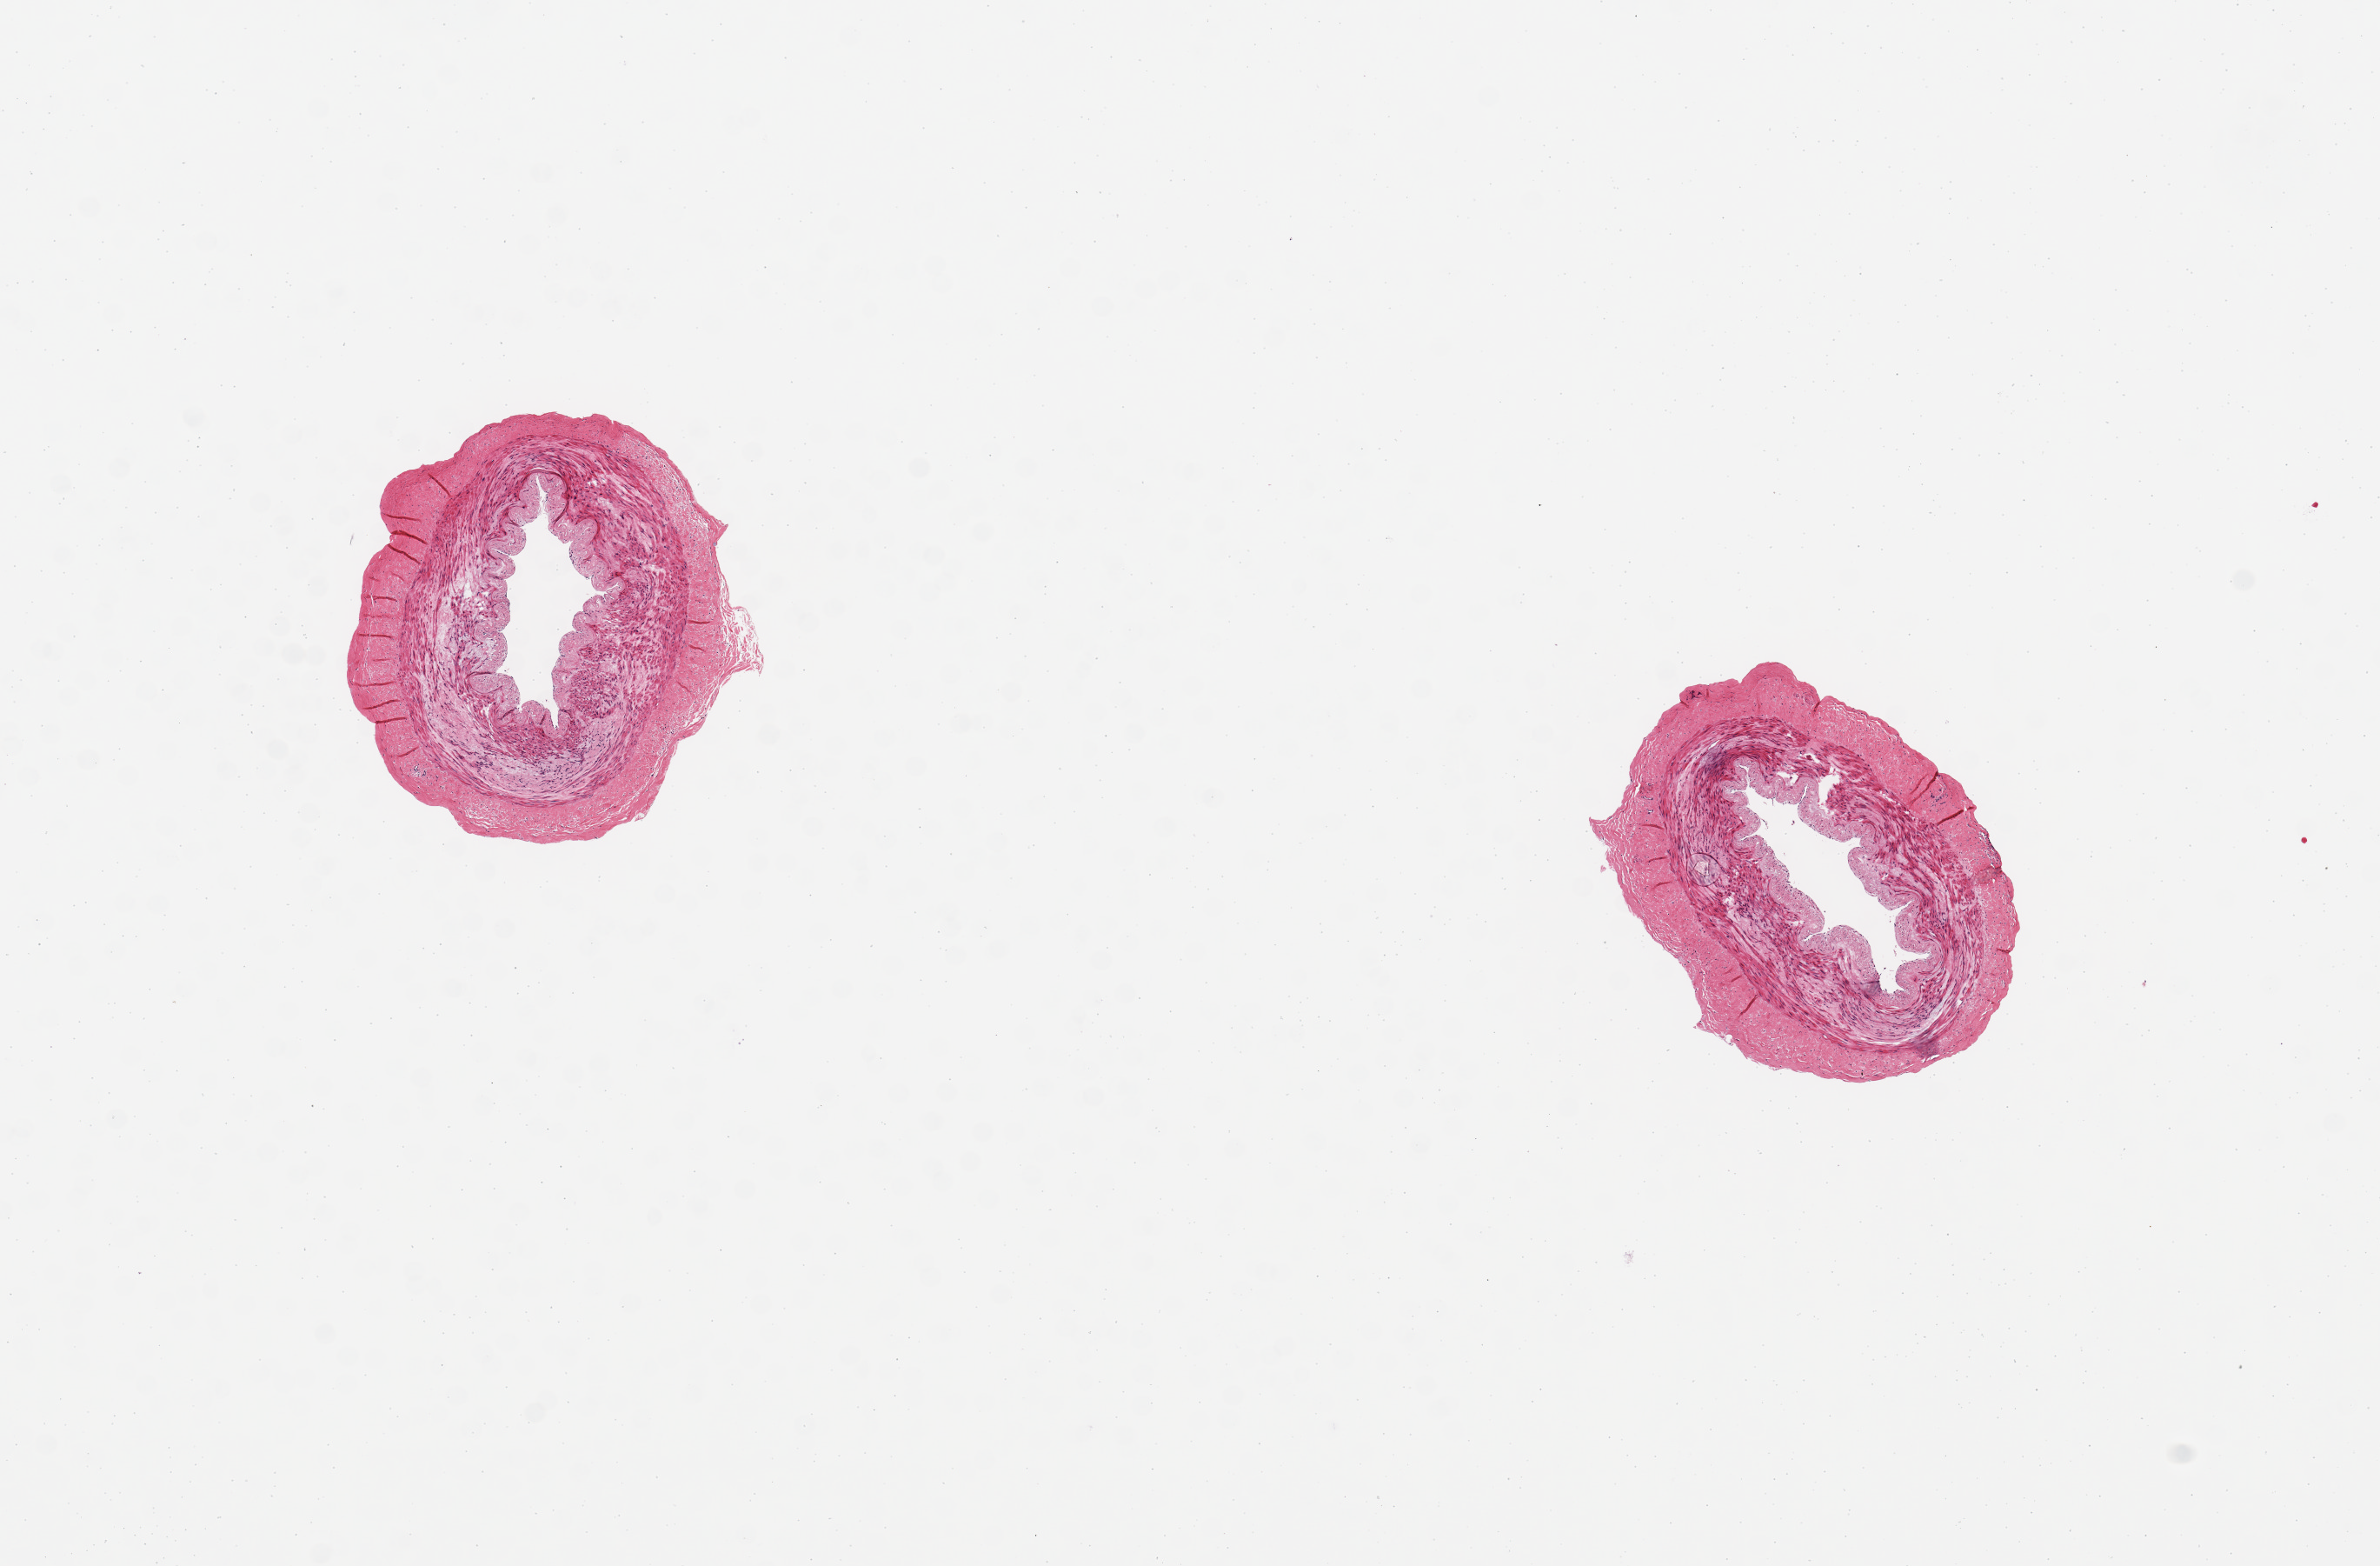
H&E whole-slide image — whole scanned area (about 10.8 x 7.1 mm, slide scanned at 20x) shown as a low-resolution overview; PAXgene-fixed, paraffin-embedded tissue; sampled site (target tissue): tibial artery; donor tissue sample. Donor sex: male.
Reviewer comment on this tissue sample: 2 pieces, each 2mm arteries with no sclerosis or adherent adipose [good clean specimens].